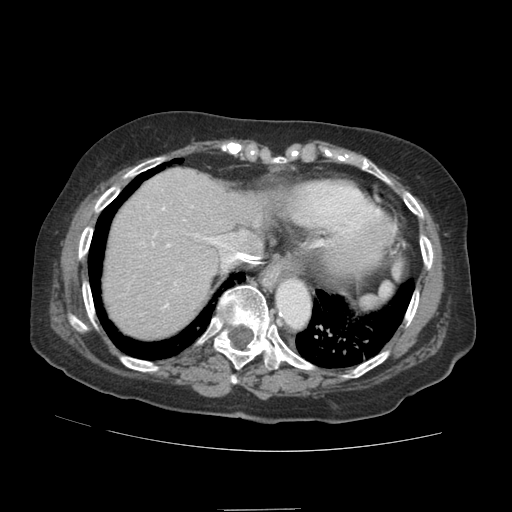
Contrast-enhanced abdominal CT (liver protocol), one axial slice. Slice 75 of 89 in the series (ordered by position). 140 kVp. Soft-tissue window (W 400 / L 40 HU). 2.5 mm slice thickness. 512 × 512 image matrix. Case-level facts recorded for this patient, not image findings: diagnosis: hepatocellular carcinoma (patient treated with transarterial chemoembolisation; whether this scan precedes or follows treatment is not stated here); TNM stage (as recorded): Stage-II; Child-Pugh class: A.
Annotated regions visible in this slice (semi-automatically segmented with operator editing):
- abdominal aorta: bounding box <277,281,309,327> (left, top, right, bottom; pixels)
- liver parenchyma outside the tumour (the mass and vessels are separate outlines, so this box may not span the whole liver): <104,168,270,338>
- liver vessels: <152,205,234,308>